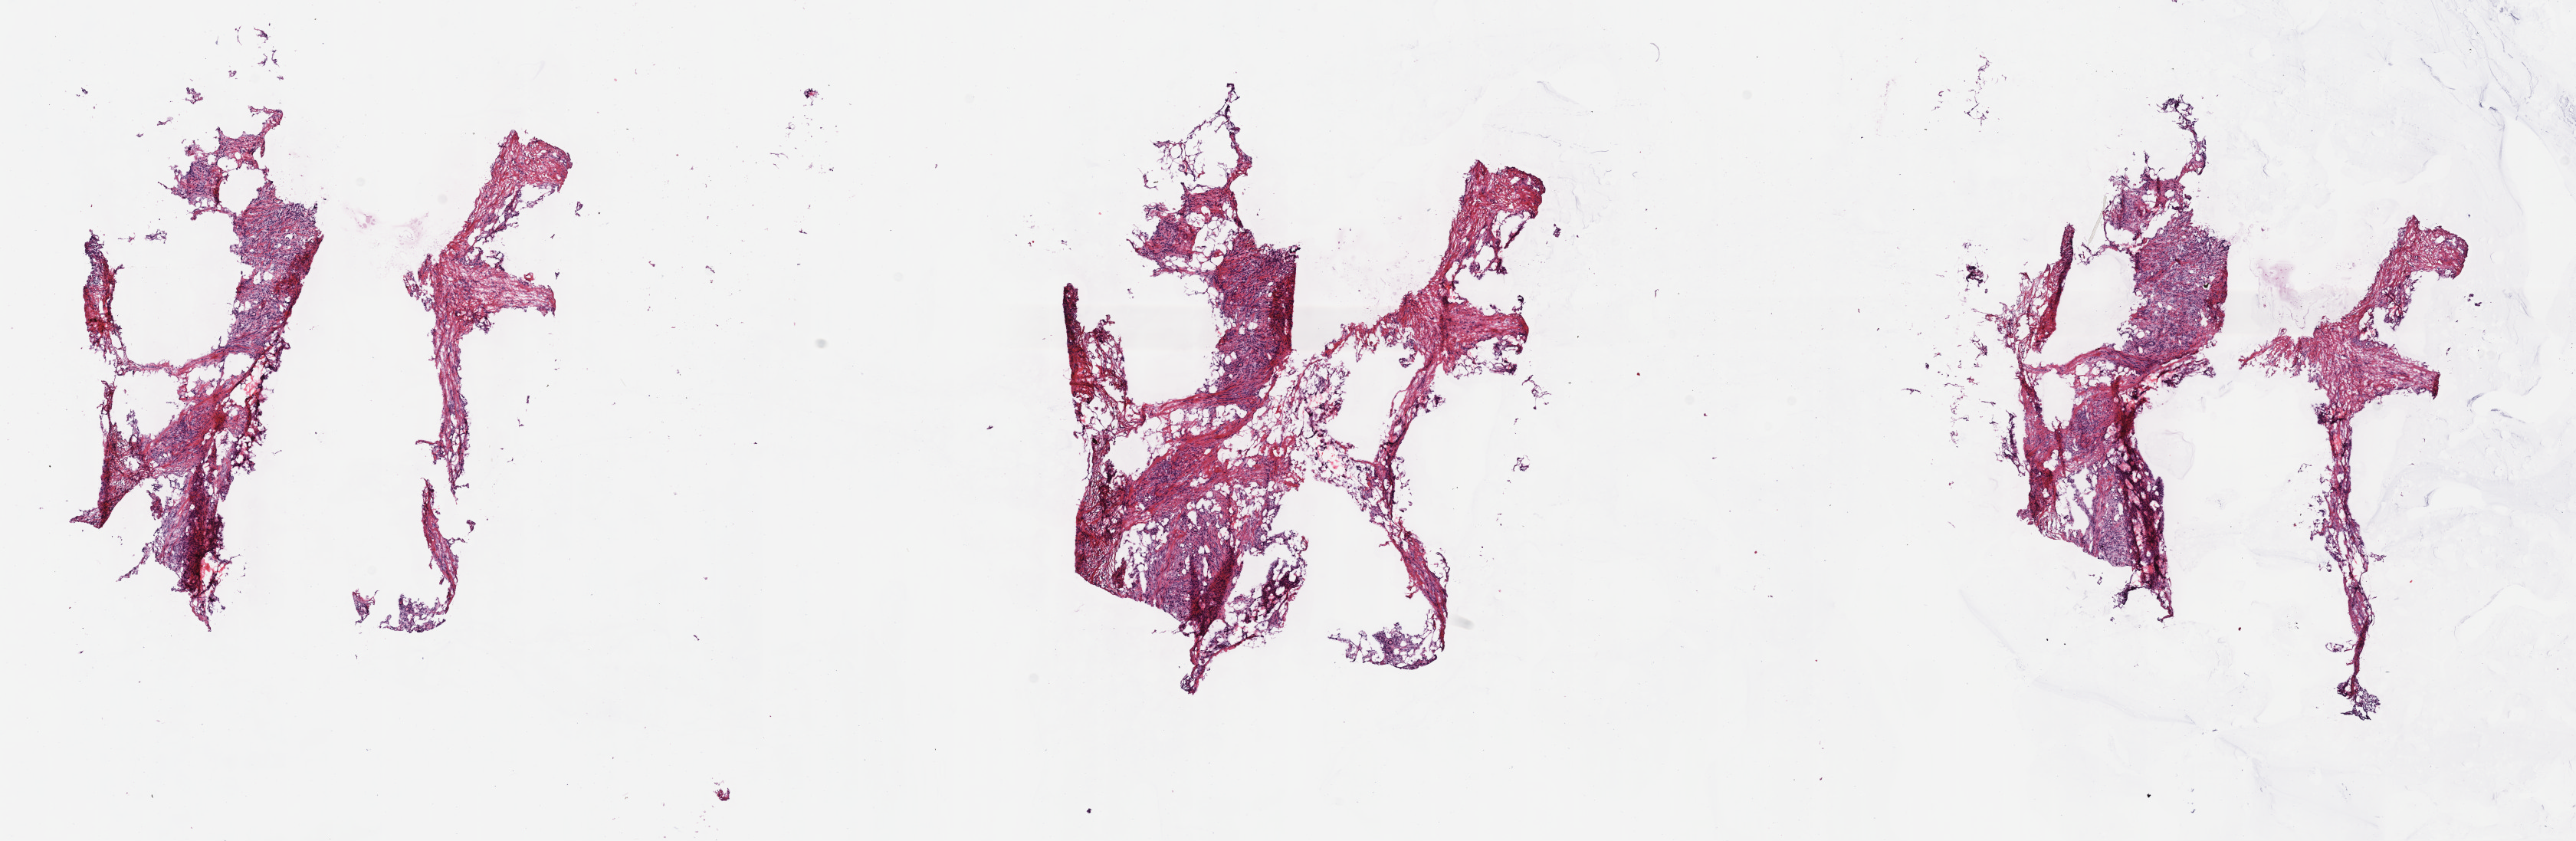
Digitized Hematoxylin and eosin (H&E) stained tissue section (whole slide), a low-resolution overview of the entire scanned area, about 27.2 x 8.9 mm, frozen section, breast, primary tumour sample. Patient: female, age at initial diagnosis 68 years. Composition of this section per pathologist review: tumour cells 100%, tumour nuclei 65%, normal cells 0%, stromal cells 0%, necrosis 0%. Infiltration values recorded for this section: lymphocyte infiltration 3%, monocyte infiltration 0%, neutrophil infiltration 0%.
Laterality: left. TNM: T3 N0 MX. AJCC pathologic stage: IIB (7th edition). Lymph nodes positive (case pathology): 0 of 11 examined. Histologic diagnosis: Lobular carcinoma, NOS.